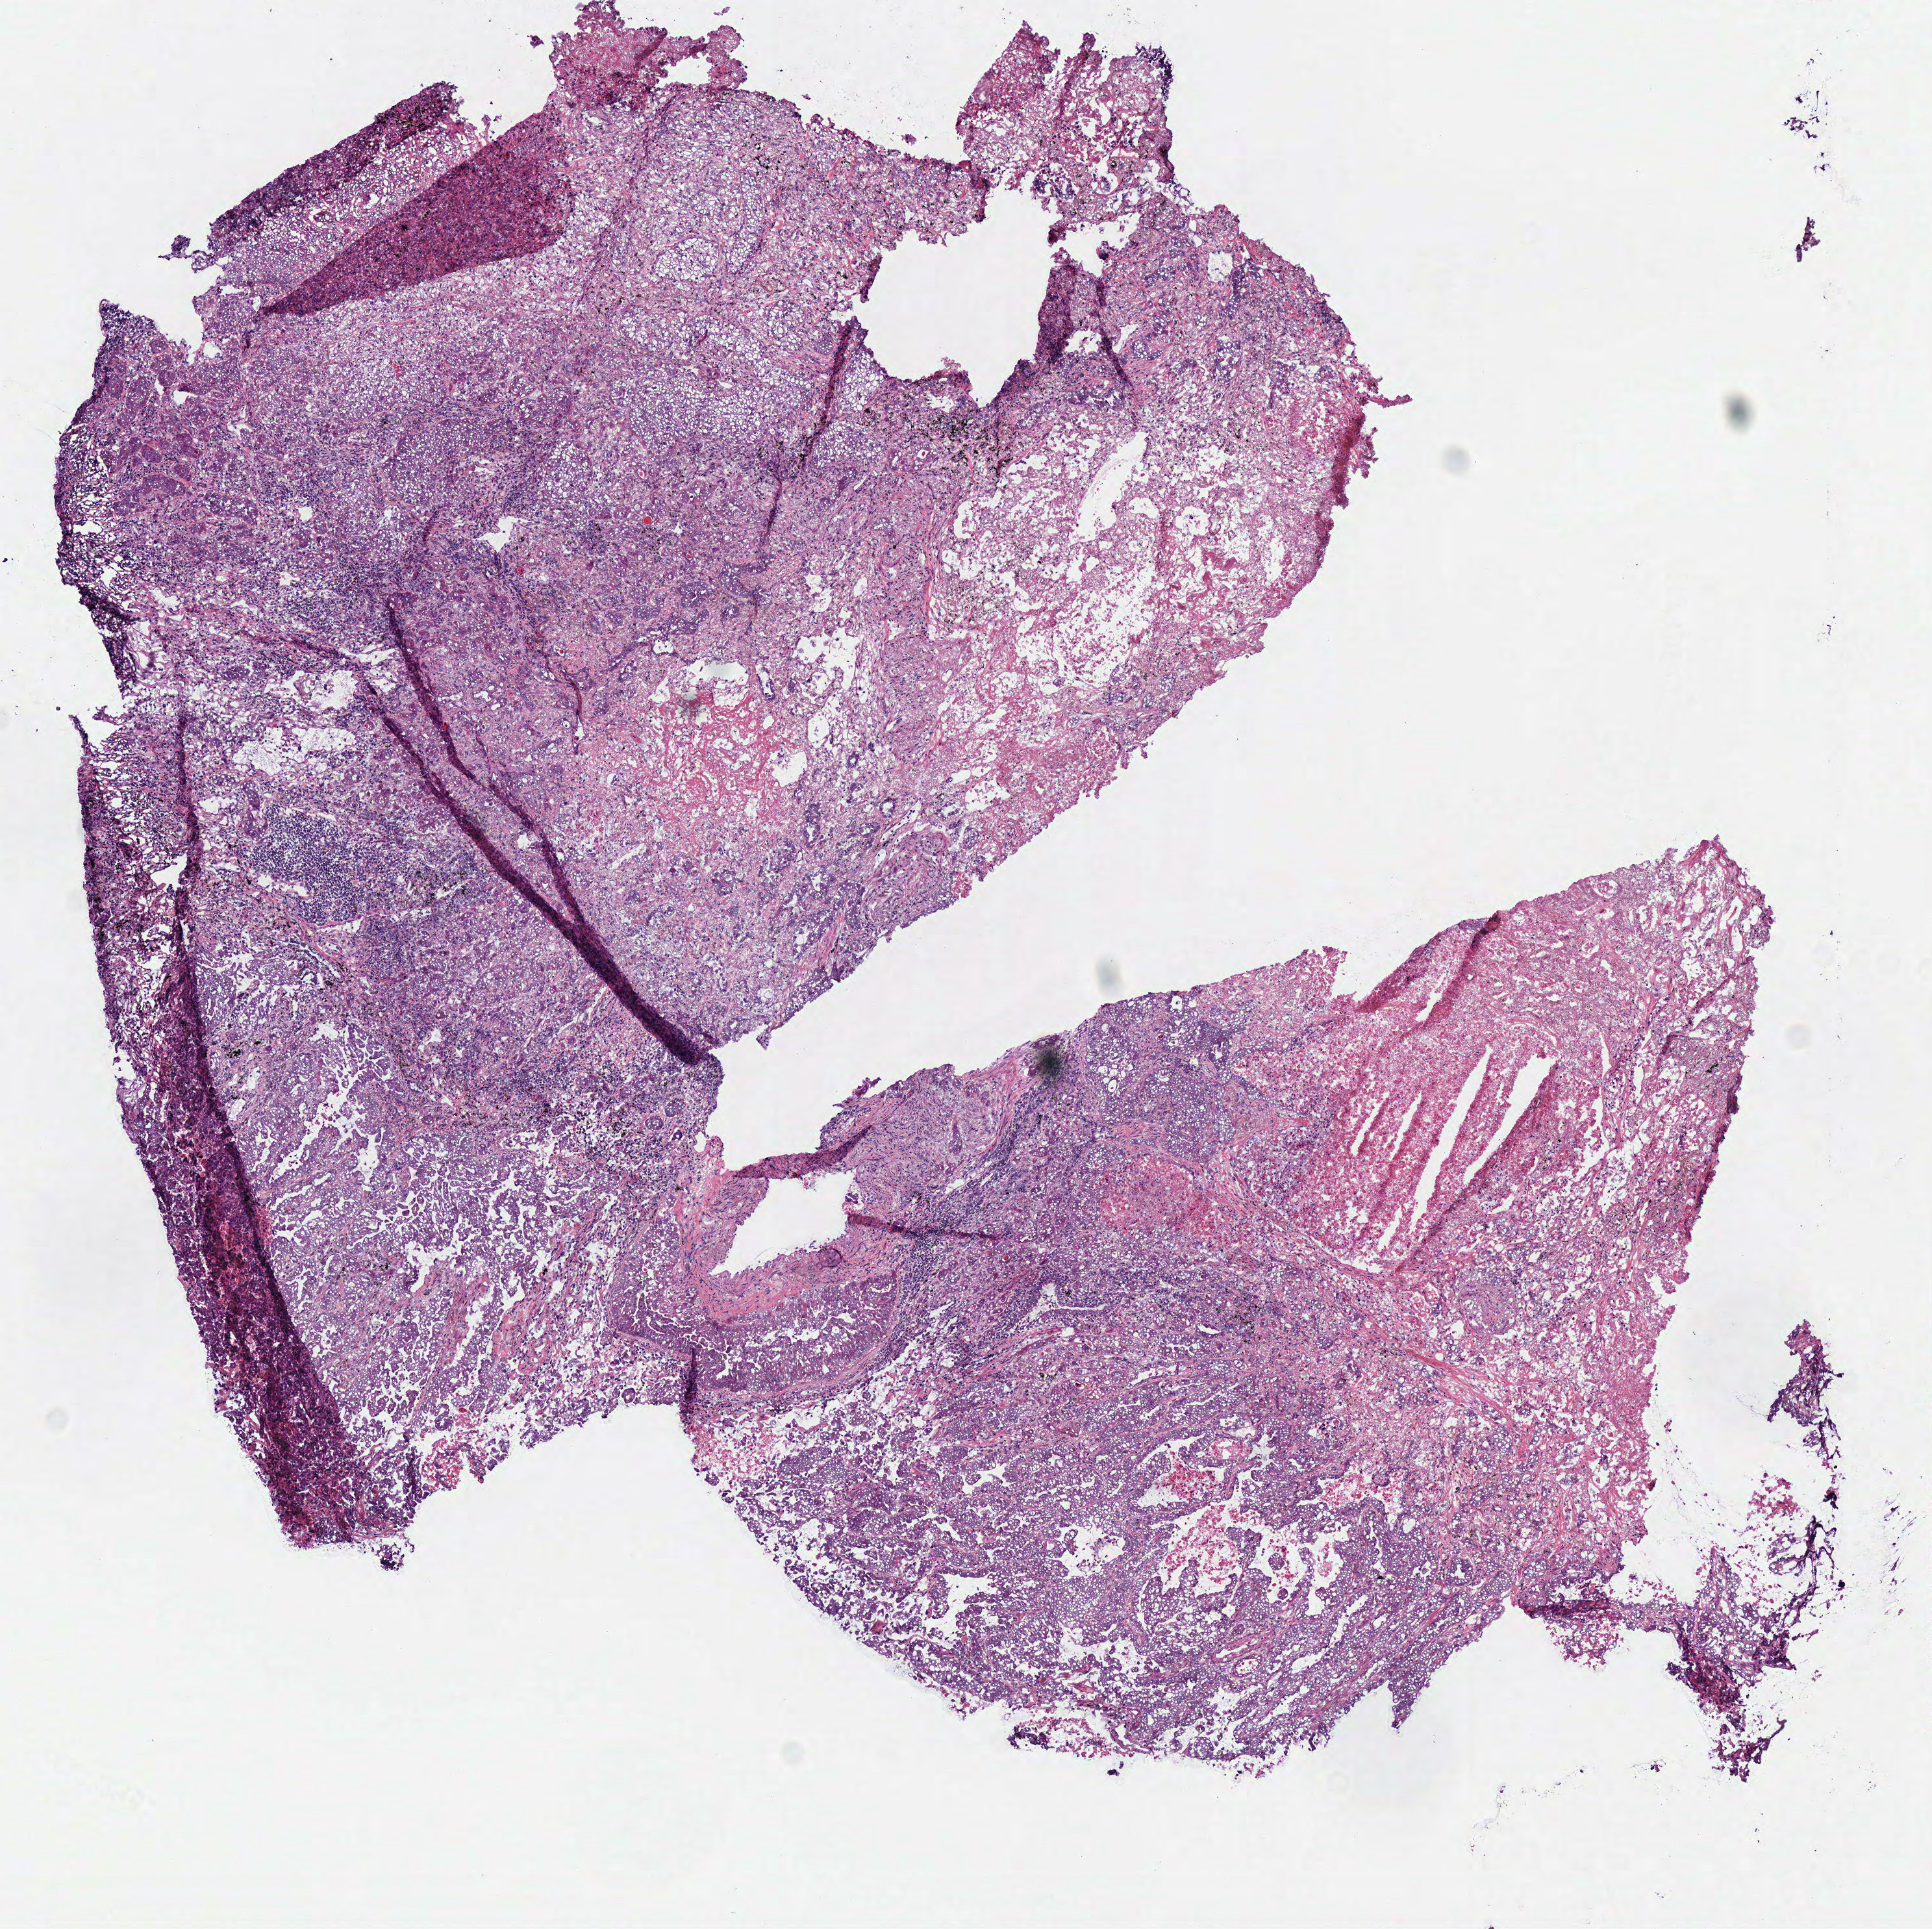
Whole-slide histology image, H&E — a low-resolution overview of the entire scanned area, about 5.9 x 5.8 mm (slide scanned at 40x), frozen section, primary tumour sample from the lung. Female patient; age at initial diagnosis 65 years. Pathologist review of this section (percent, as recorded): tumour cells 65%, tumour nuclei 75%, normal cells 0%, stromal cells 10%, necrosis 25%.
- AJCC pathologic stage: IIA (5th edition)
- histologic diagnosis: Adenocarcinoma, NOS (upper lobe, lung)
- laterality: left